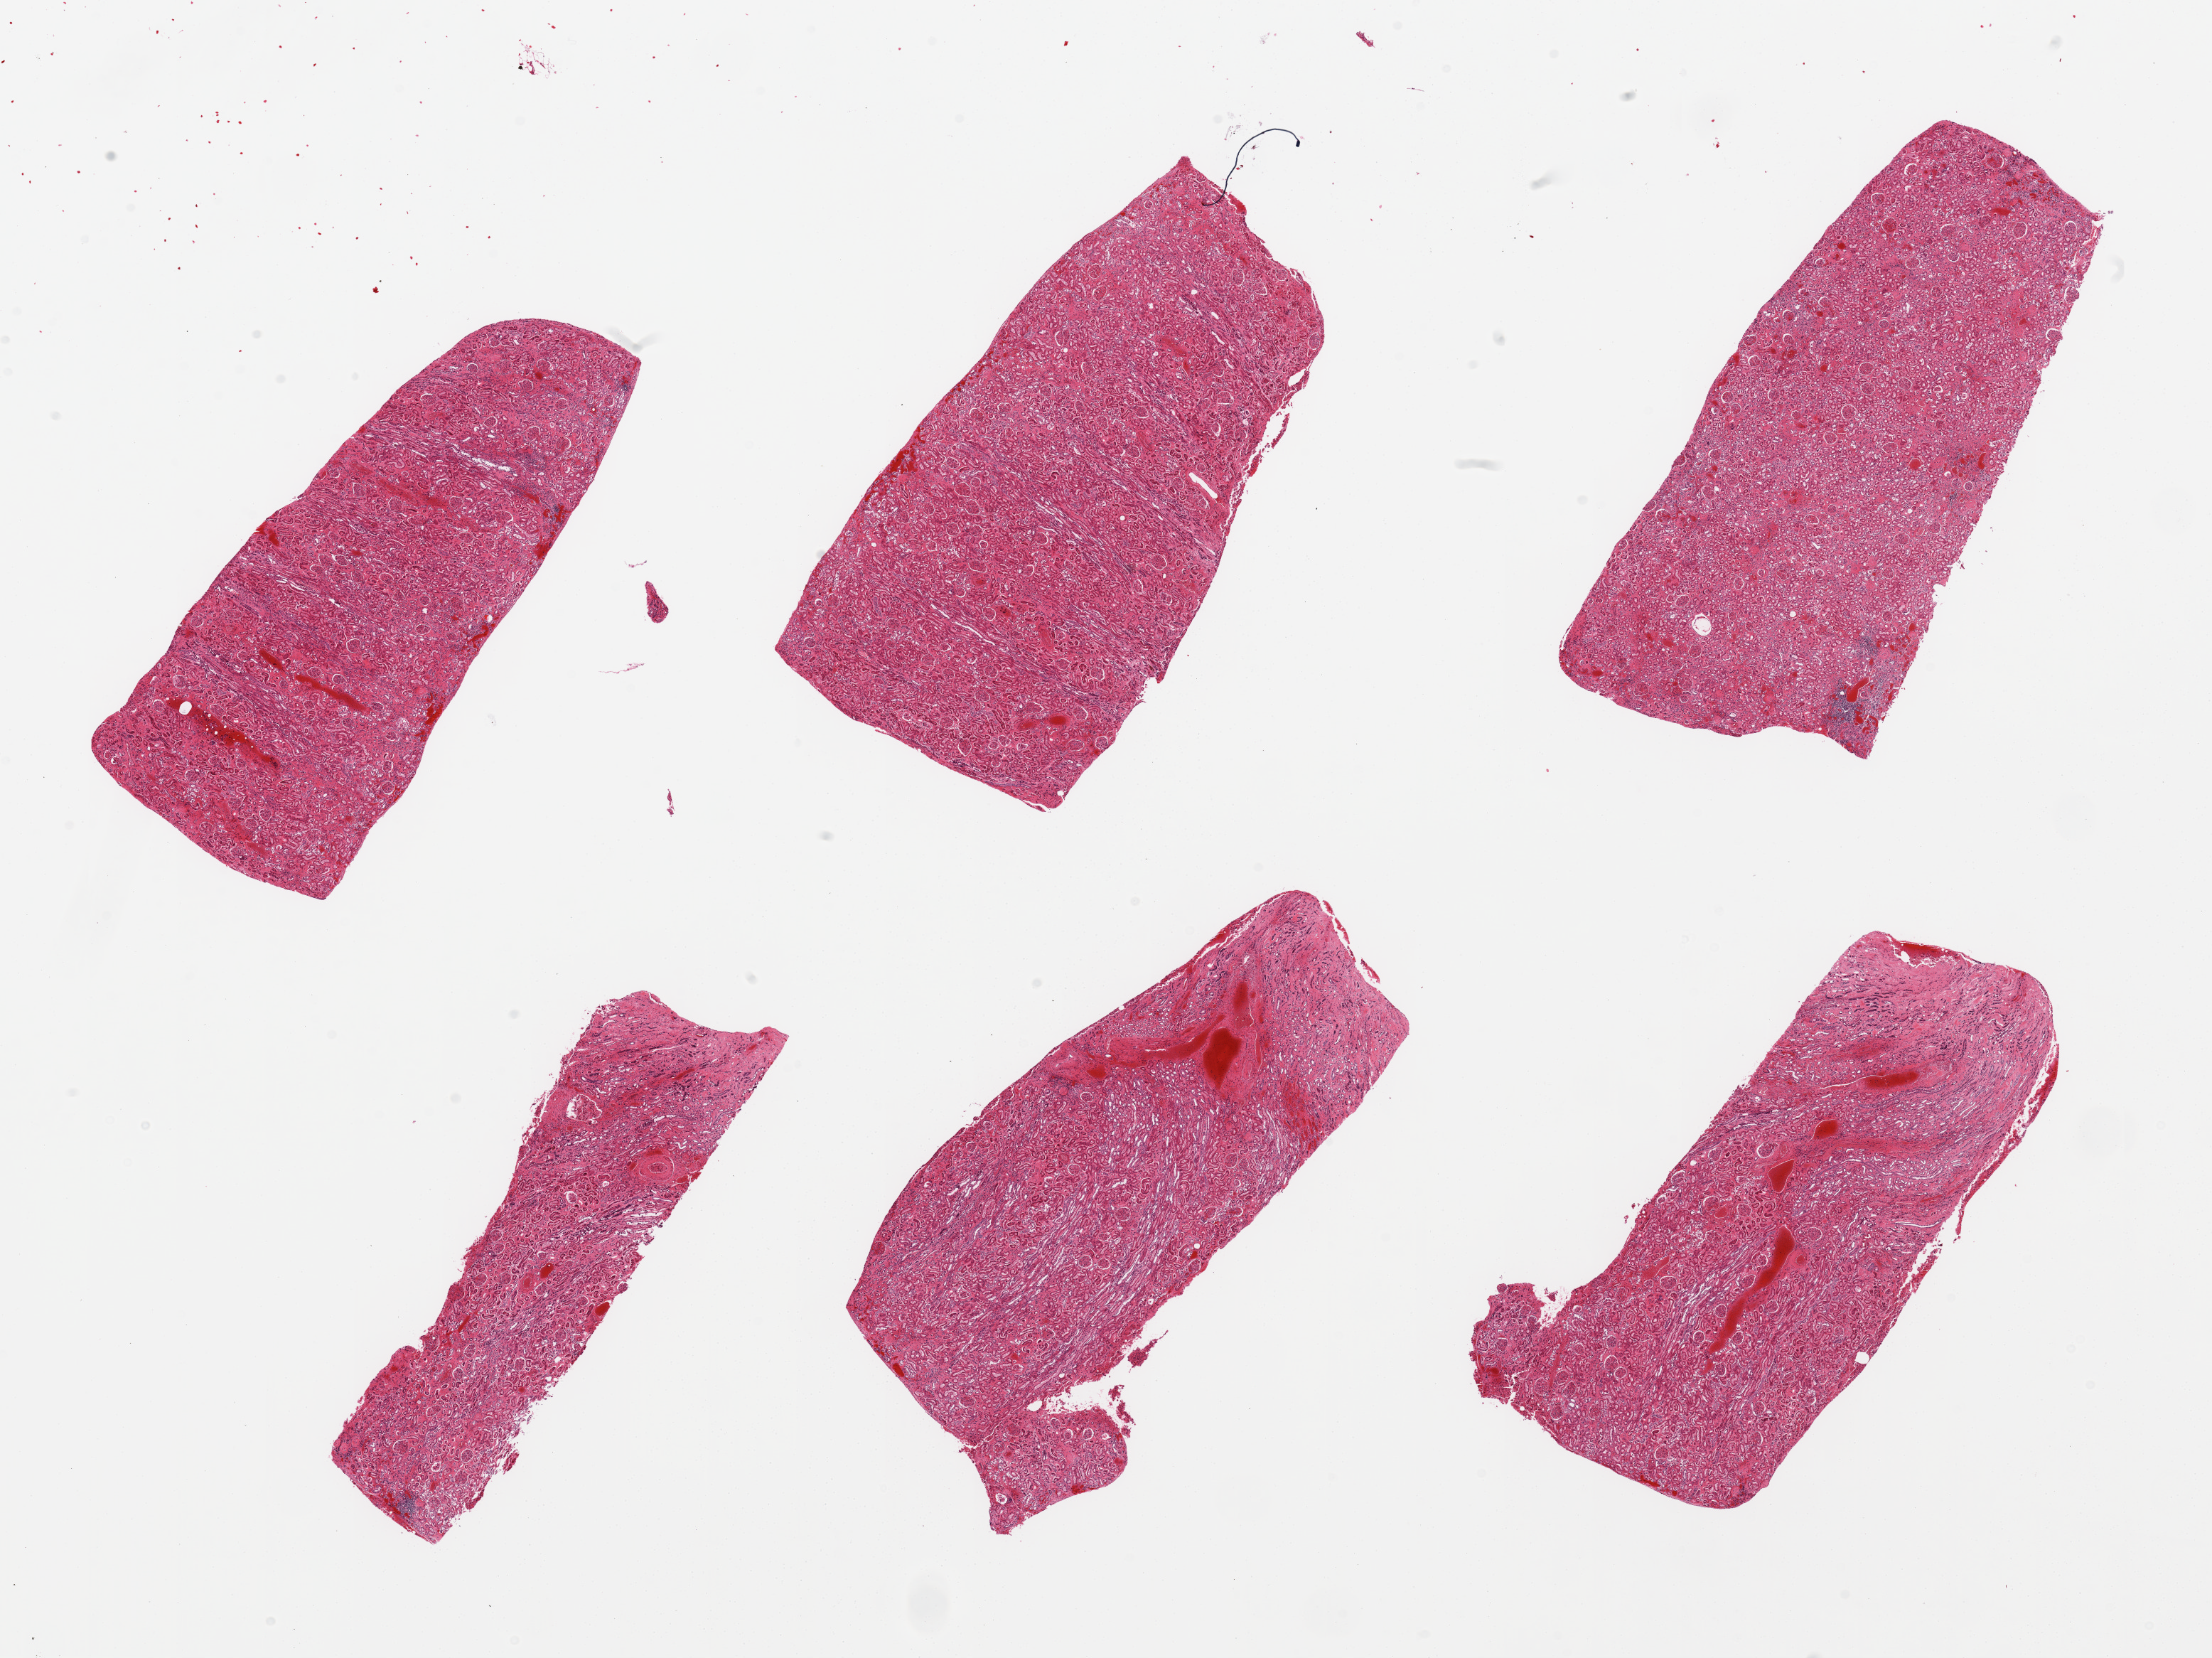
H&E whole-slide image, brightfield, low-resolution overview of the scanned area, about 24.6 x 18.4 mm (slide scanned at 20x); PAXgene-fixed, paraffin-embedded tissue; target tissue: renal cortex; donor tissue sample. Male donor.
Reviewer comment on this tissue sample: 6 pieces, glomeruli present but badly autolyzed.